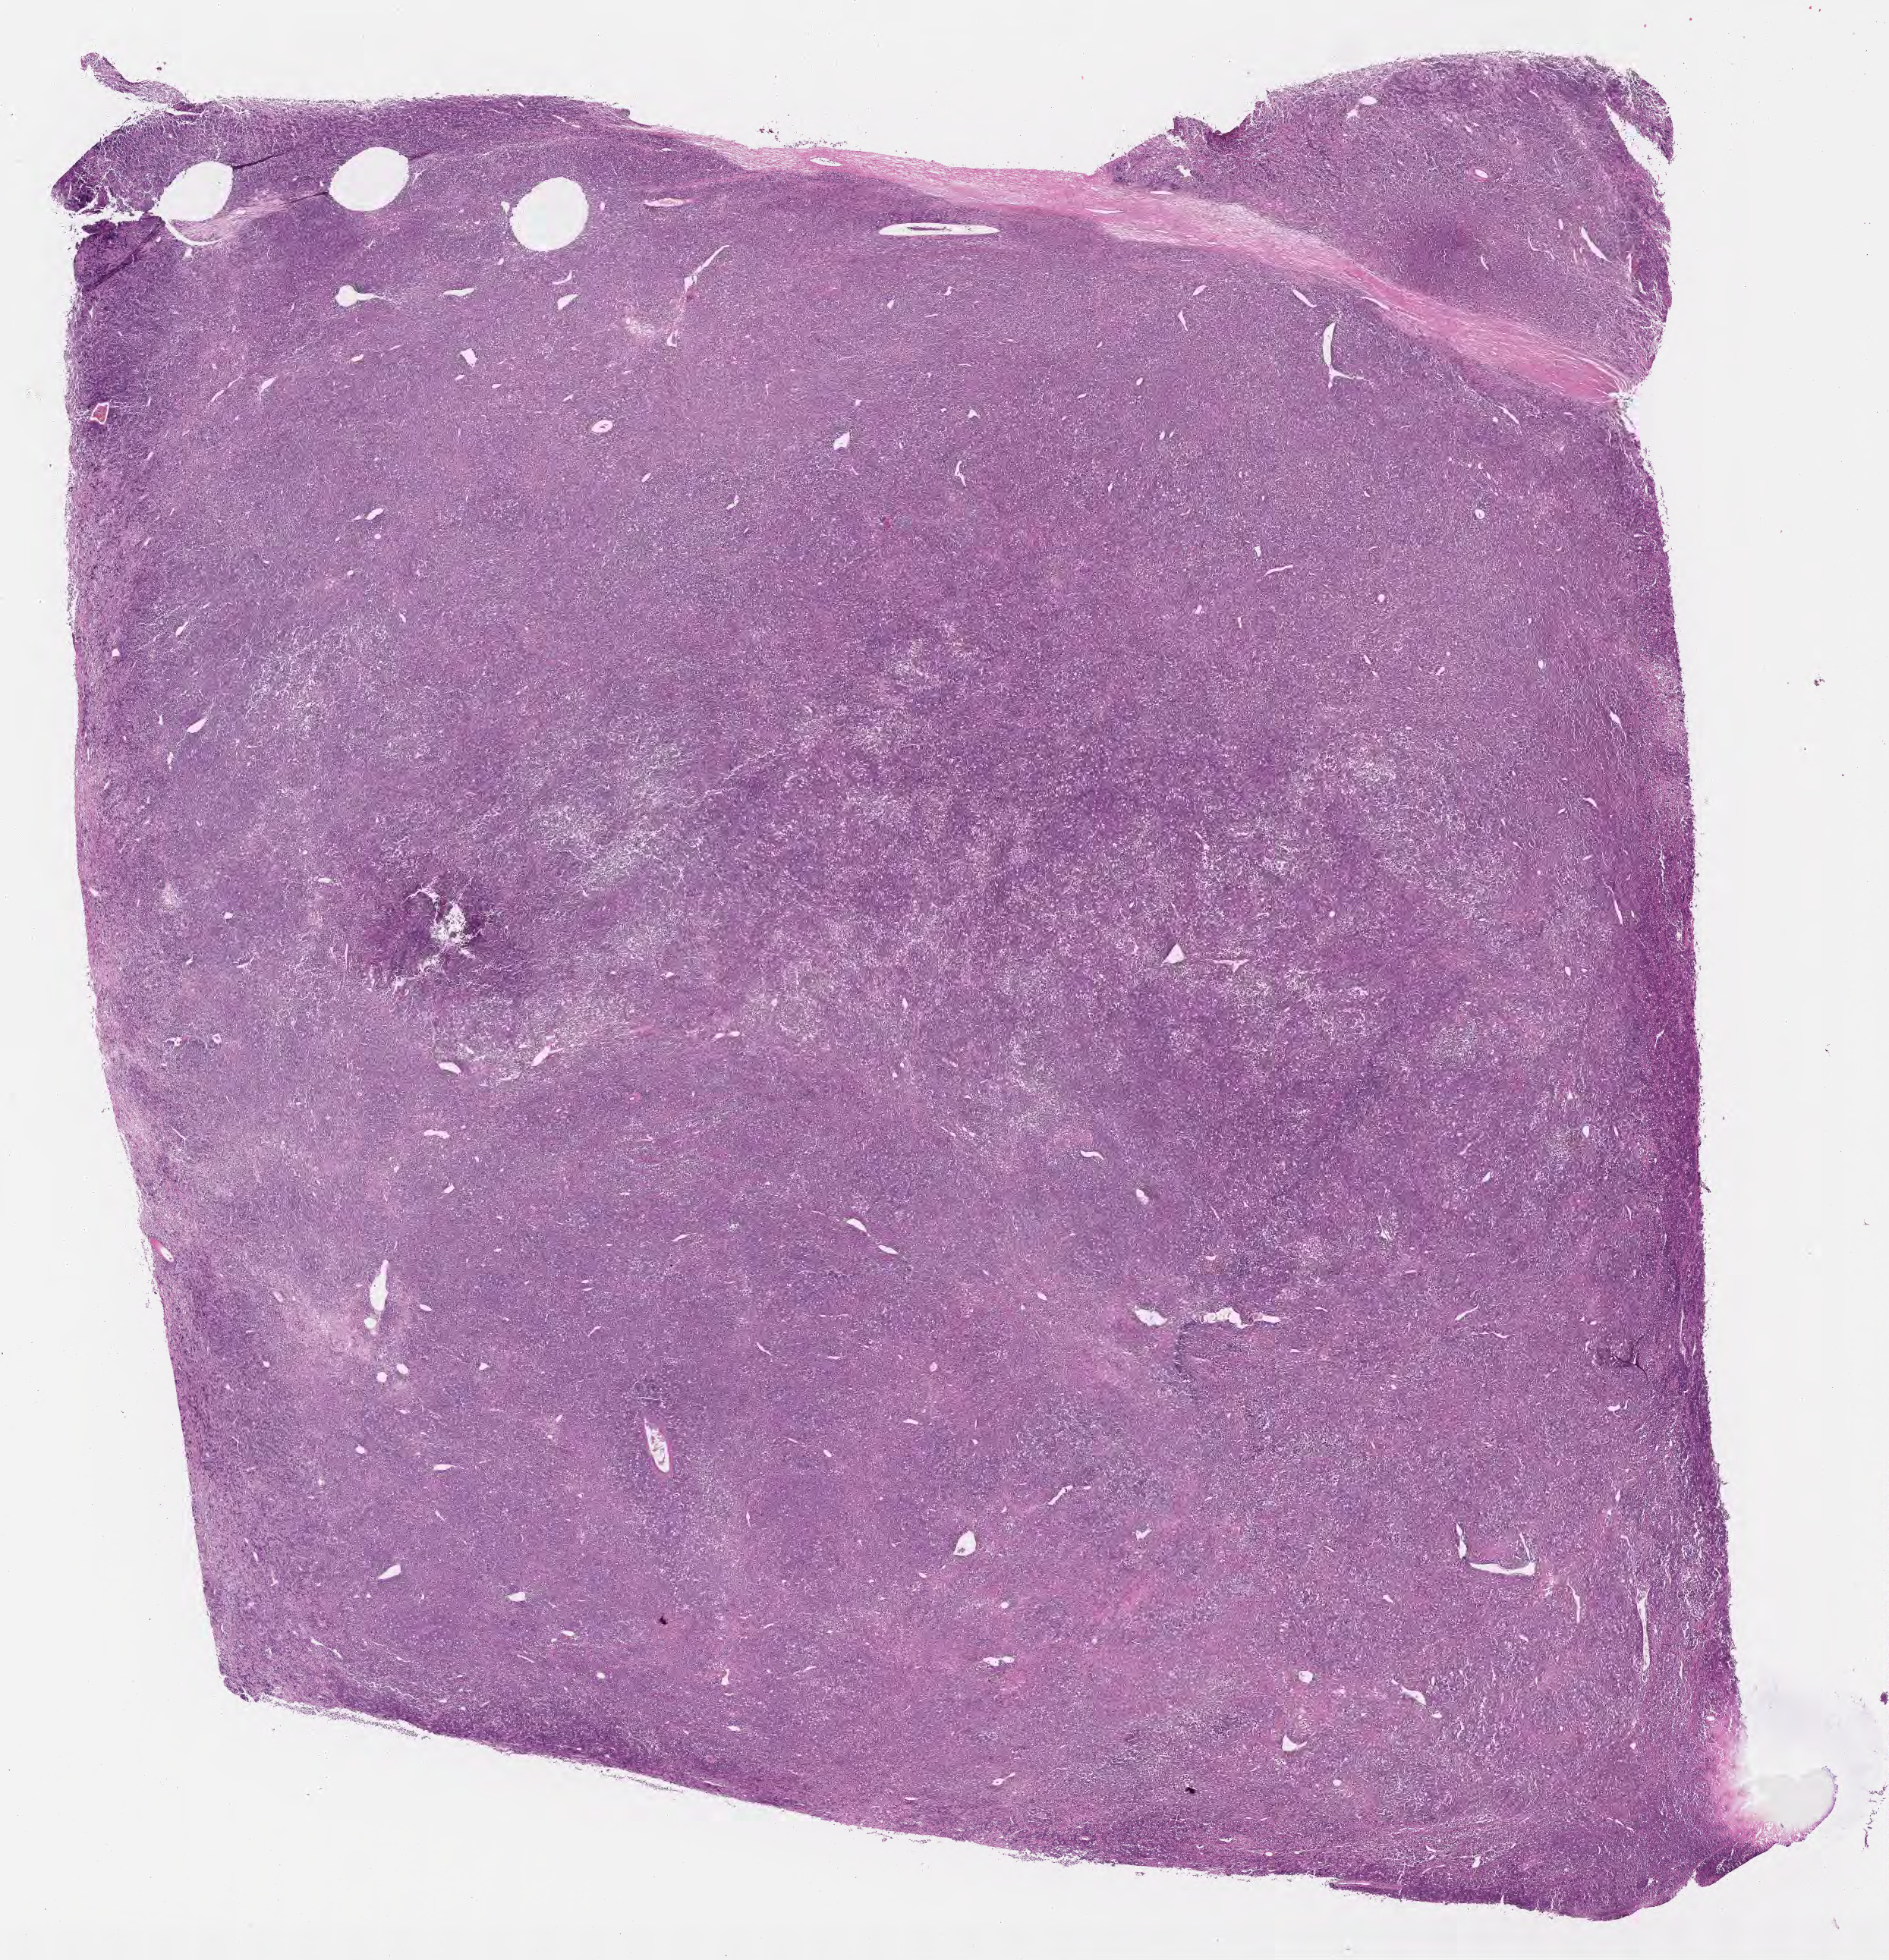
Digitized haematoxylin and eosin-stained section, low-resolution overview of the scanned area, about 20.1 x 20.9 mm. Formalin-fixed, paraffin-embedded (FFPE) tissue. Specimen: primary tumor. Female patient, aged 22. Composition of this section per pathologist review: tumor cells 90%, tumor nuclei 90%, stromal cells 5%, necrosis 5%, normal cells 0%. Infiltration values recorded for this section: lymphocyte infiltration 30%, monocyte infiltration 40%, neutrophil infiltration 5%.
Ann Arbor stage (patient): Stage IV. Histologic diagnosis: Burkitt lymphoma, NOS.